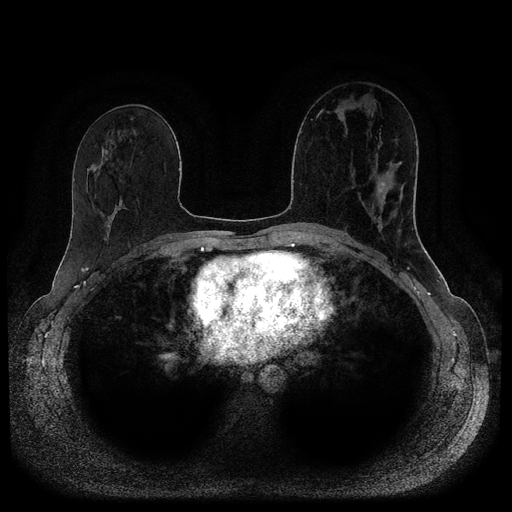
Breast MRI (dynamic contrast-enhanced, multi-phase), one axial slice. Position 53 of 116 along the scan axis. Dynamic contrast-enhanced series, time point 2 of 5 at this slice position (early post-contrast). 1.5 T. TE 2.6 ms, TR 5.3 ms. 2 mm slice thickness. 512 × 512 image matrix. Female patient, age 45 years.
Annotated regions visible in this slice (semi-automatically segmented with operator editing):
- breast lesion (labelled 'tumour' in the annotation; benign lesions carry a separate 'benign' label): box from (x=377, y=182) to (x=386, y=194) px